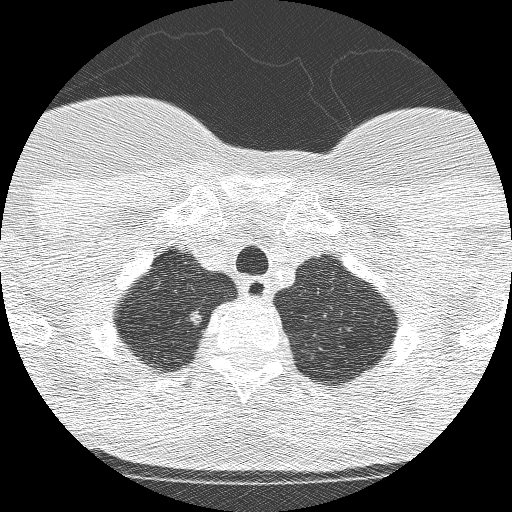
Axial slice from a low-dose chest CT screening exam; second annual screen; lung window (W 1500 / L -600 HU); 1.25 mm slice thickness; slice 217 of 250 in the series. Female participant, aged 61 years at enrolment.
Expert-annotated lung lesion, bounding box (x1, y1, x2, y2) in pixels: (162, 299, 213, 339). The exam's reader record, not a measurement of the box and not confirmed to be the same lesion: non-calcified nodule or mass ≥4 mm, right upper lobe, 11 × 8 mm, poorly defined margins, mixed attenuation, pre-existing on the prior screen: yes; interval growth: yes. Later outcome: lung cancer diagnosed 28 days after this screen — adenocarcinoma, NOS, right upper lobe, poorly differentiated (G3), 12 mm at pathology.